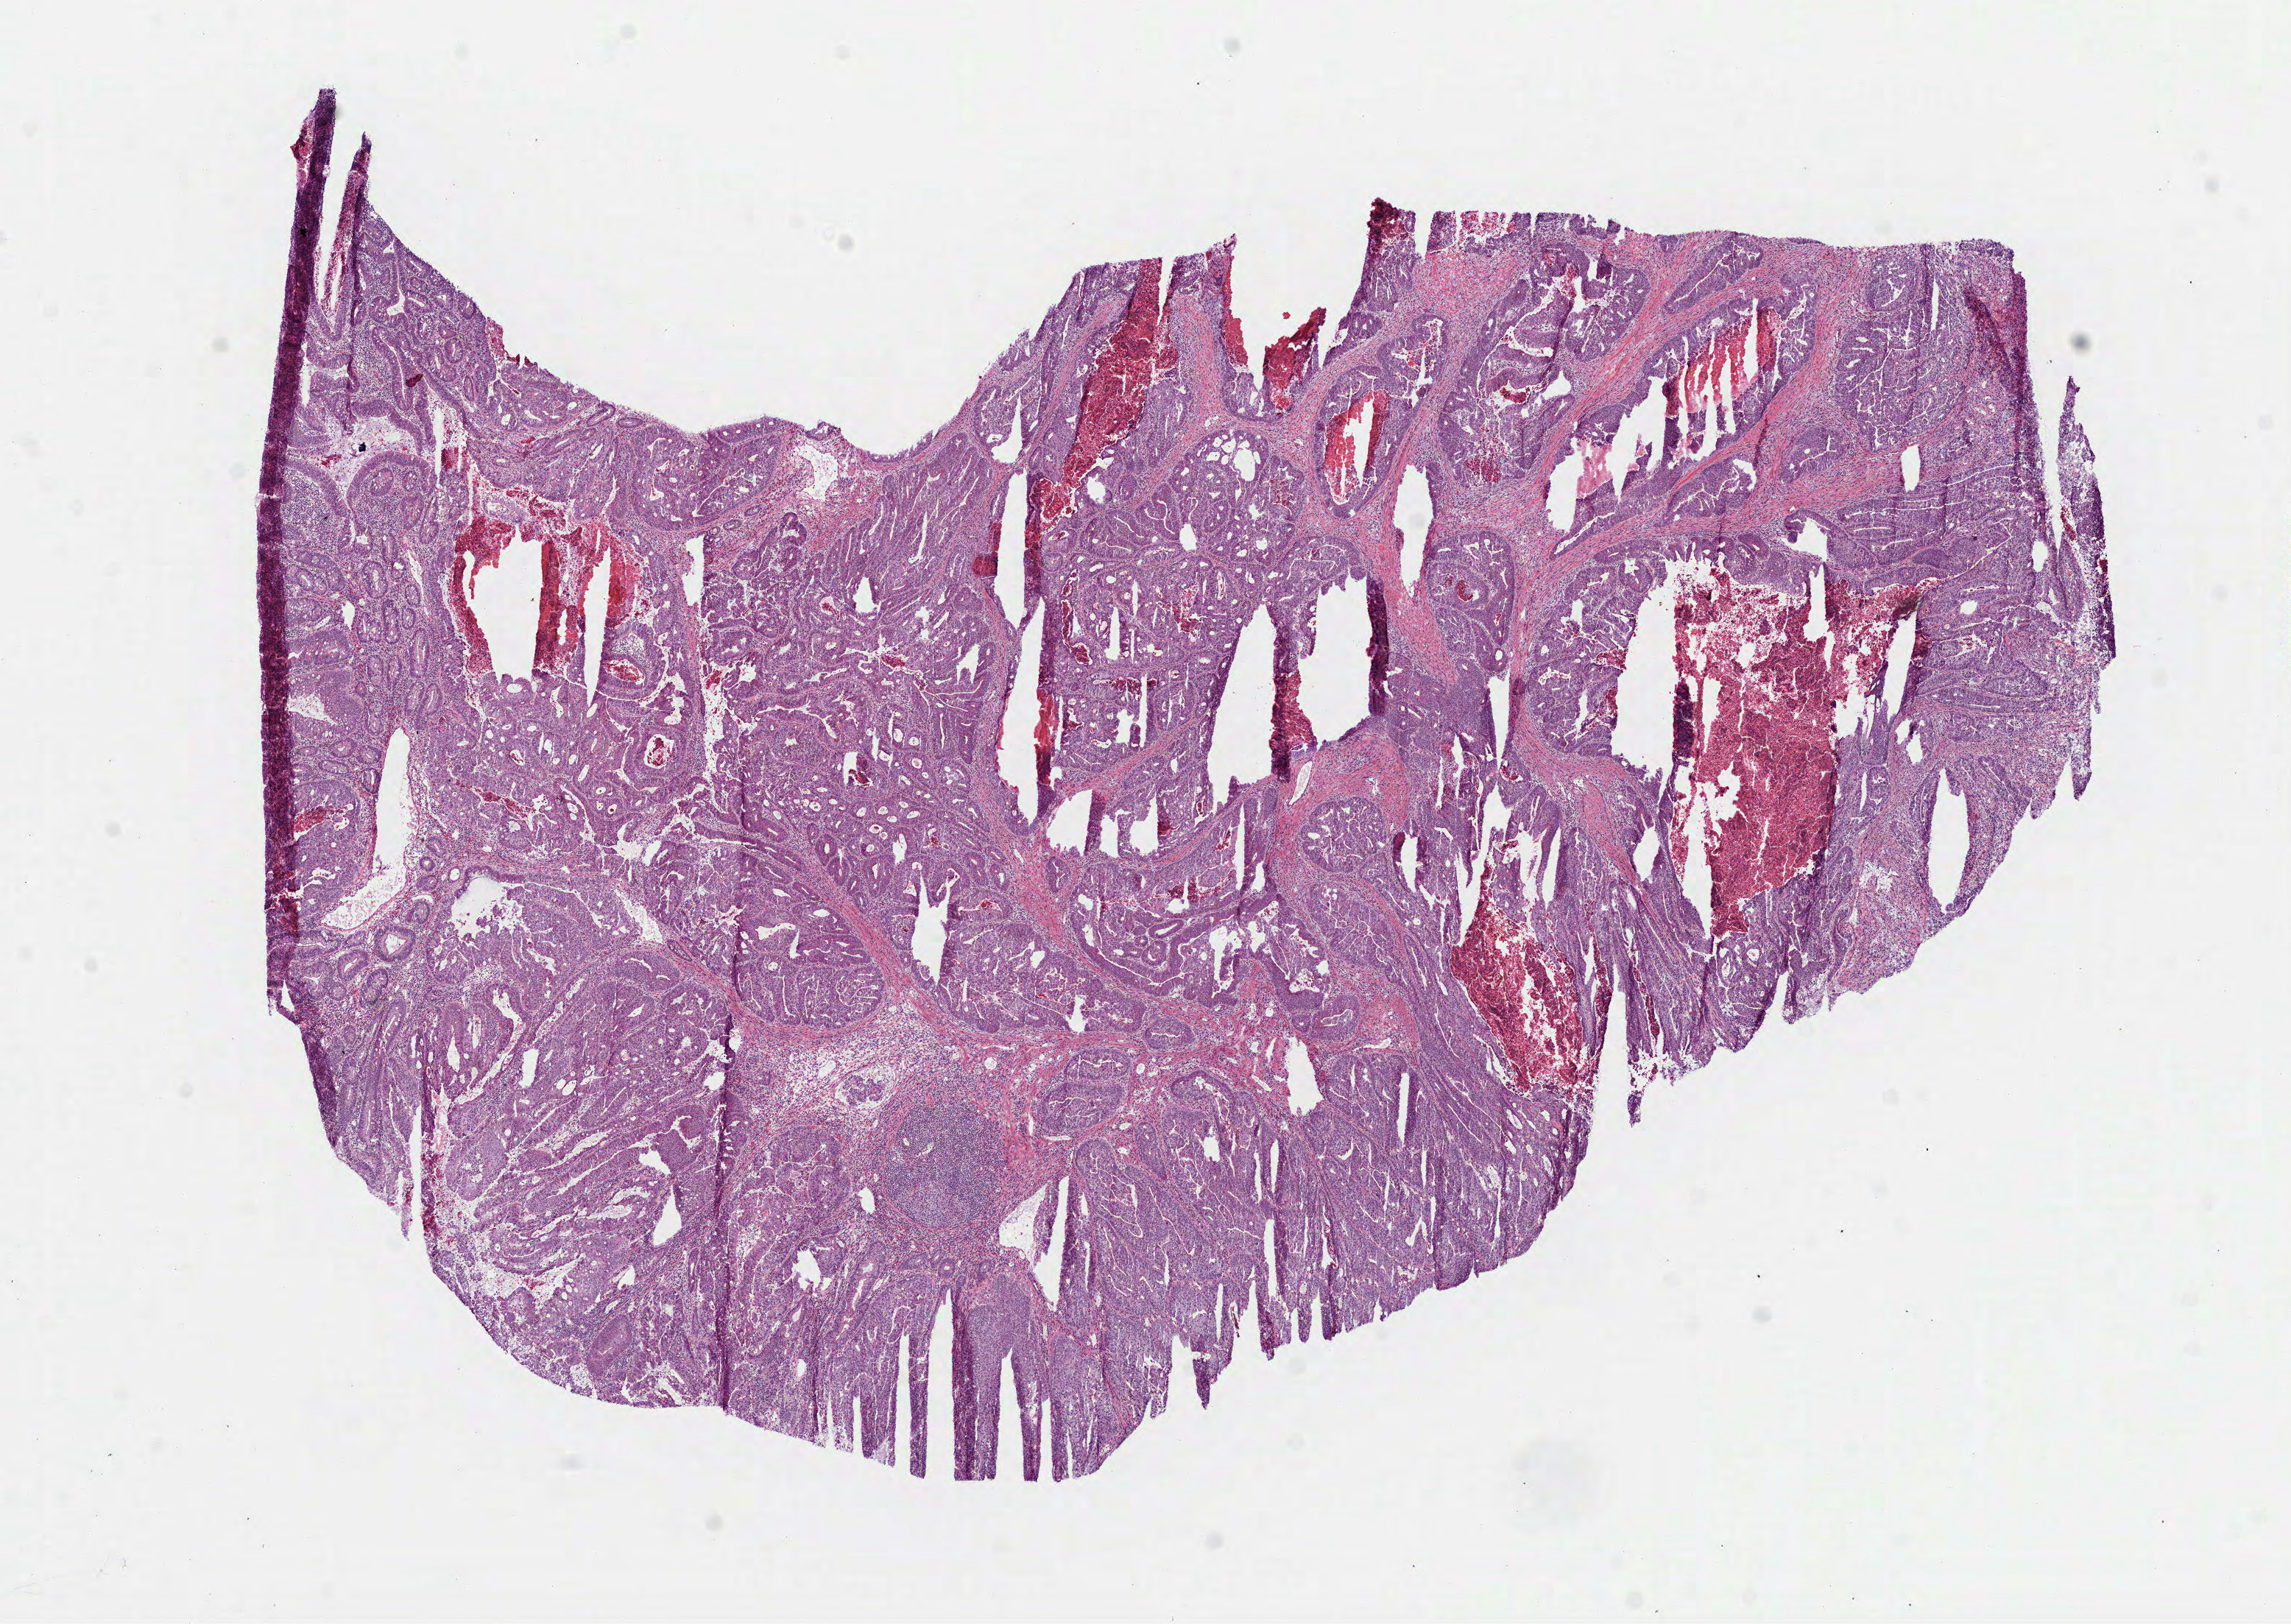
Hematoxylin and eosin (H&E) stained whole-slide image — whole scanned area (about 12.5 x 8.9 mm) shown as a low-resolution overview; frozen section from the bottom of the tissue portion; colon, primary tumour sample. Male patient; age at initial diagnosis 55 years. Slide review estimates, as recorded: tumour cells 80%, tumour nuclei 75%, normal cells 0%, stromal cells 0%, necrosis 20%. Infiltration values recorded for this section: lymphocyte infiltration 10%, monocyte infiltration 0%, neutrophil infiltration 10%.
• pathologic diagnosis: Adenocarcinoma, NOS (ascending colon)
• AJCC pathologic stage: IIIB